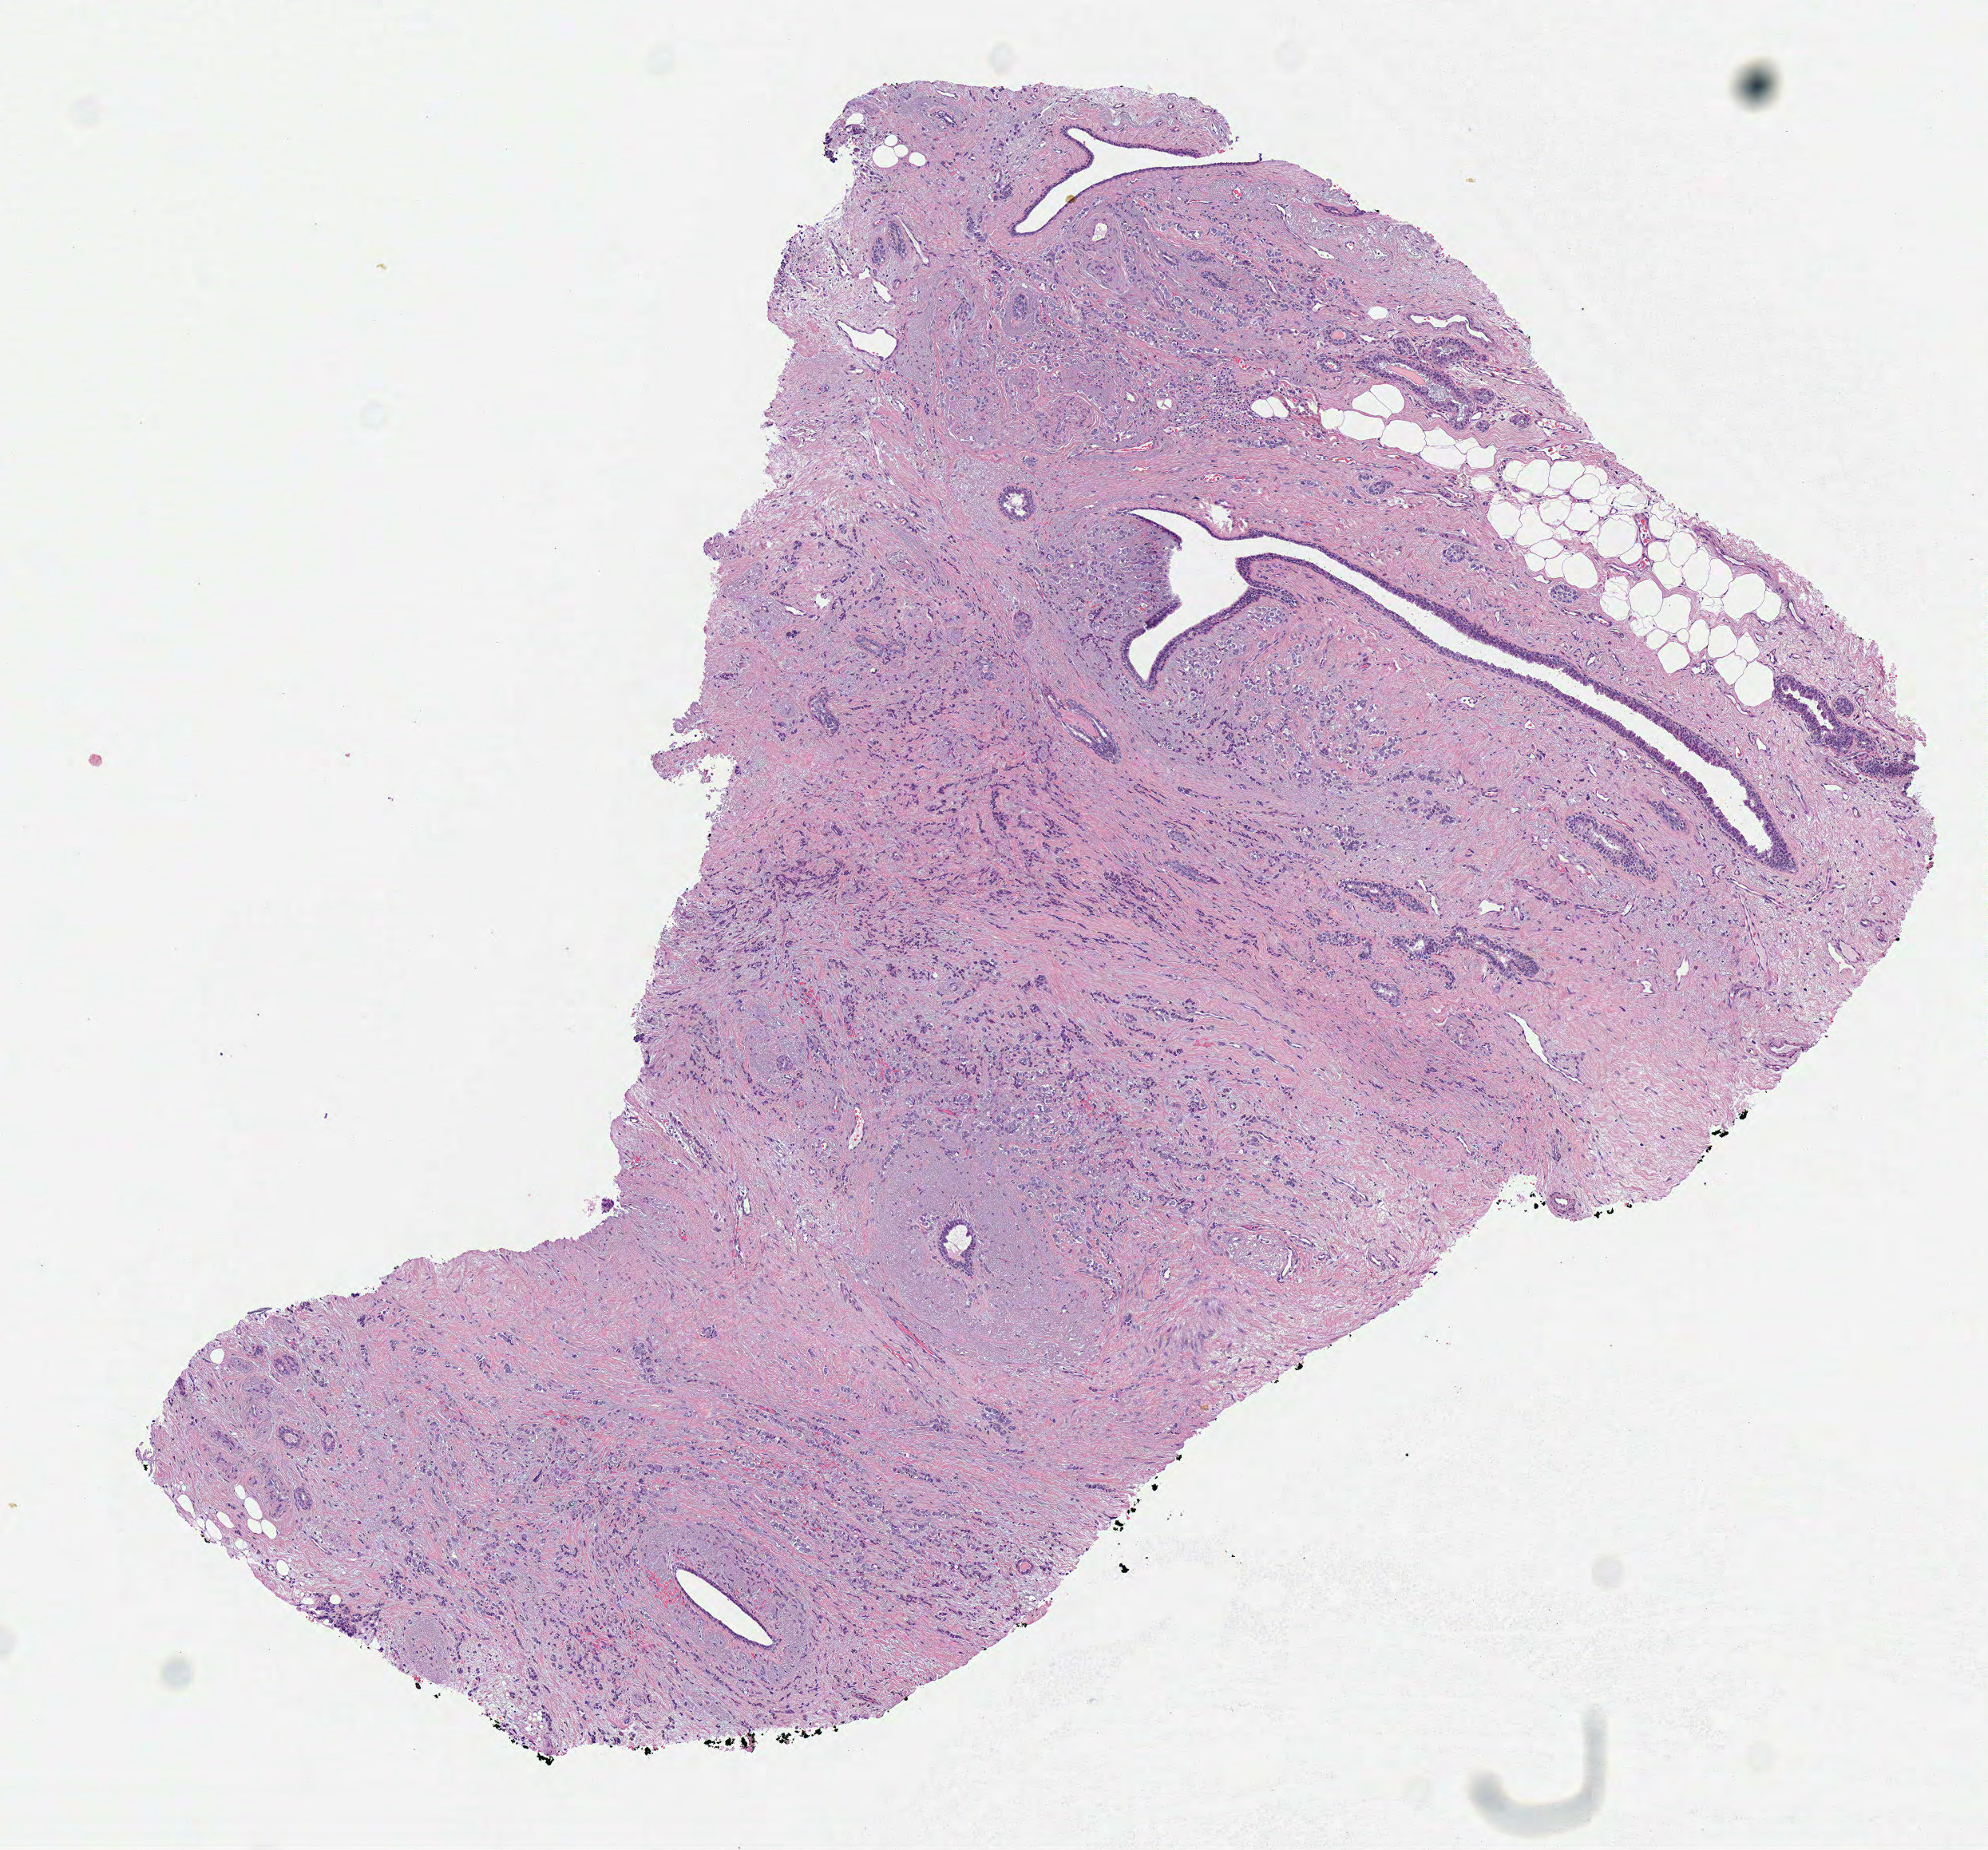
H&E whole-slide image, shown as a low-resolution overview of the whole scanned area (about 4.9 x 4.6 mm); formalin-fixed paraffin-embedded (FFPE) diagnostic section; breast, primary tumour sample. Patient: female, age at initial diagnosis 76 years.
Diagnosis: Lobular carcinoma, NOS. AJCC pathologic stage: IIA. Lymph nodes positive (case pathology): 2 of 8 examined. Laterality: right.